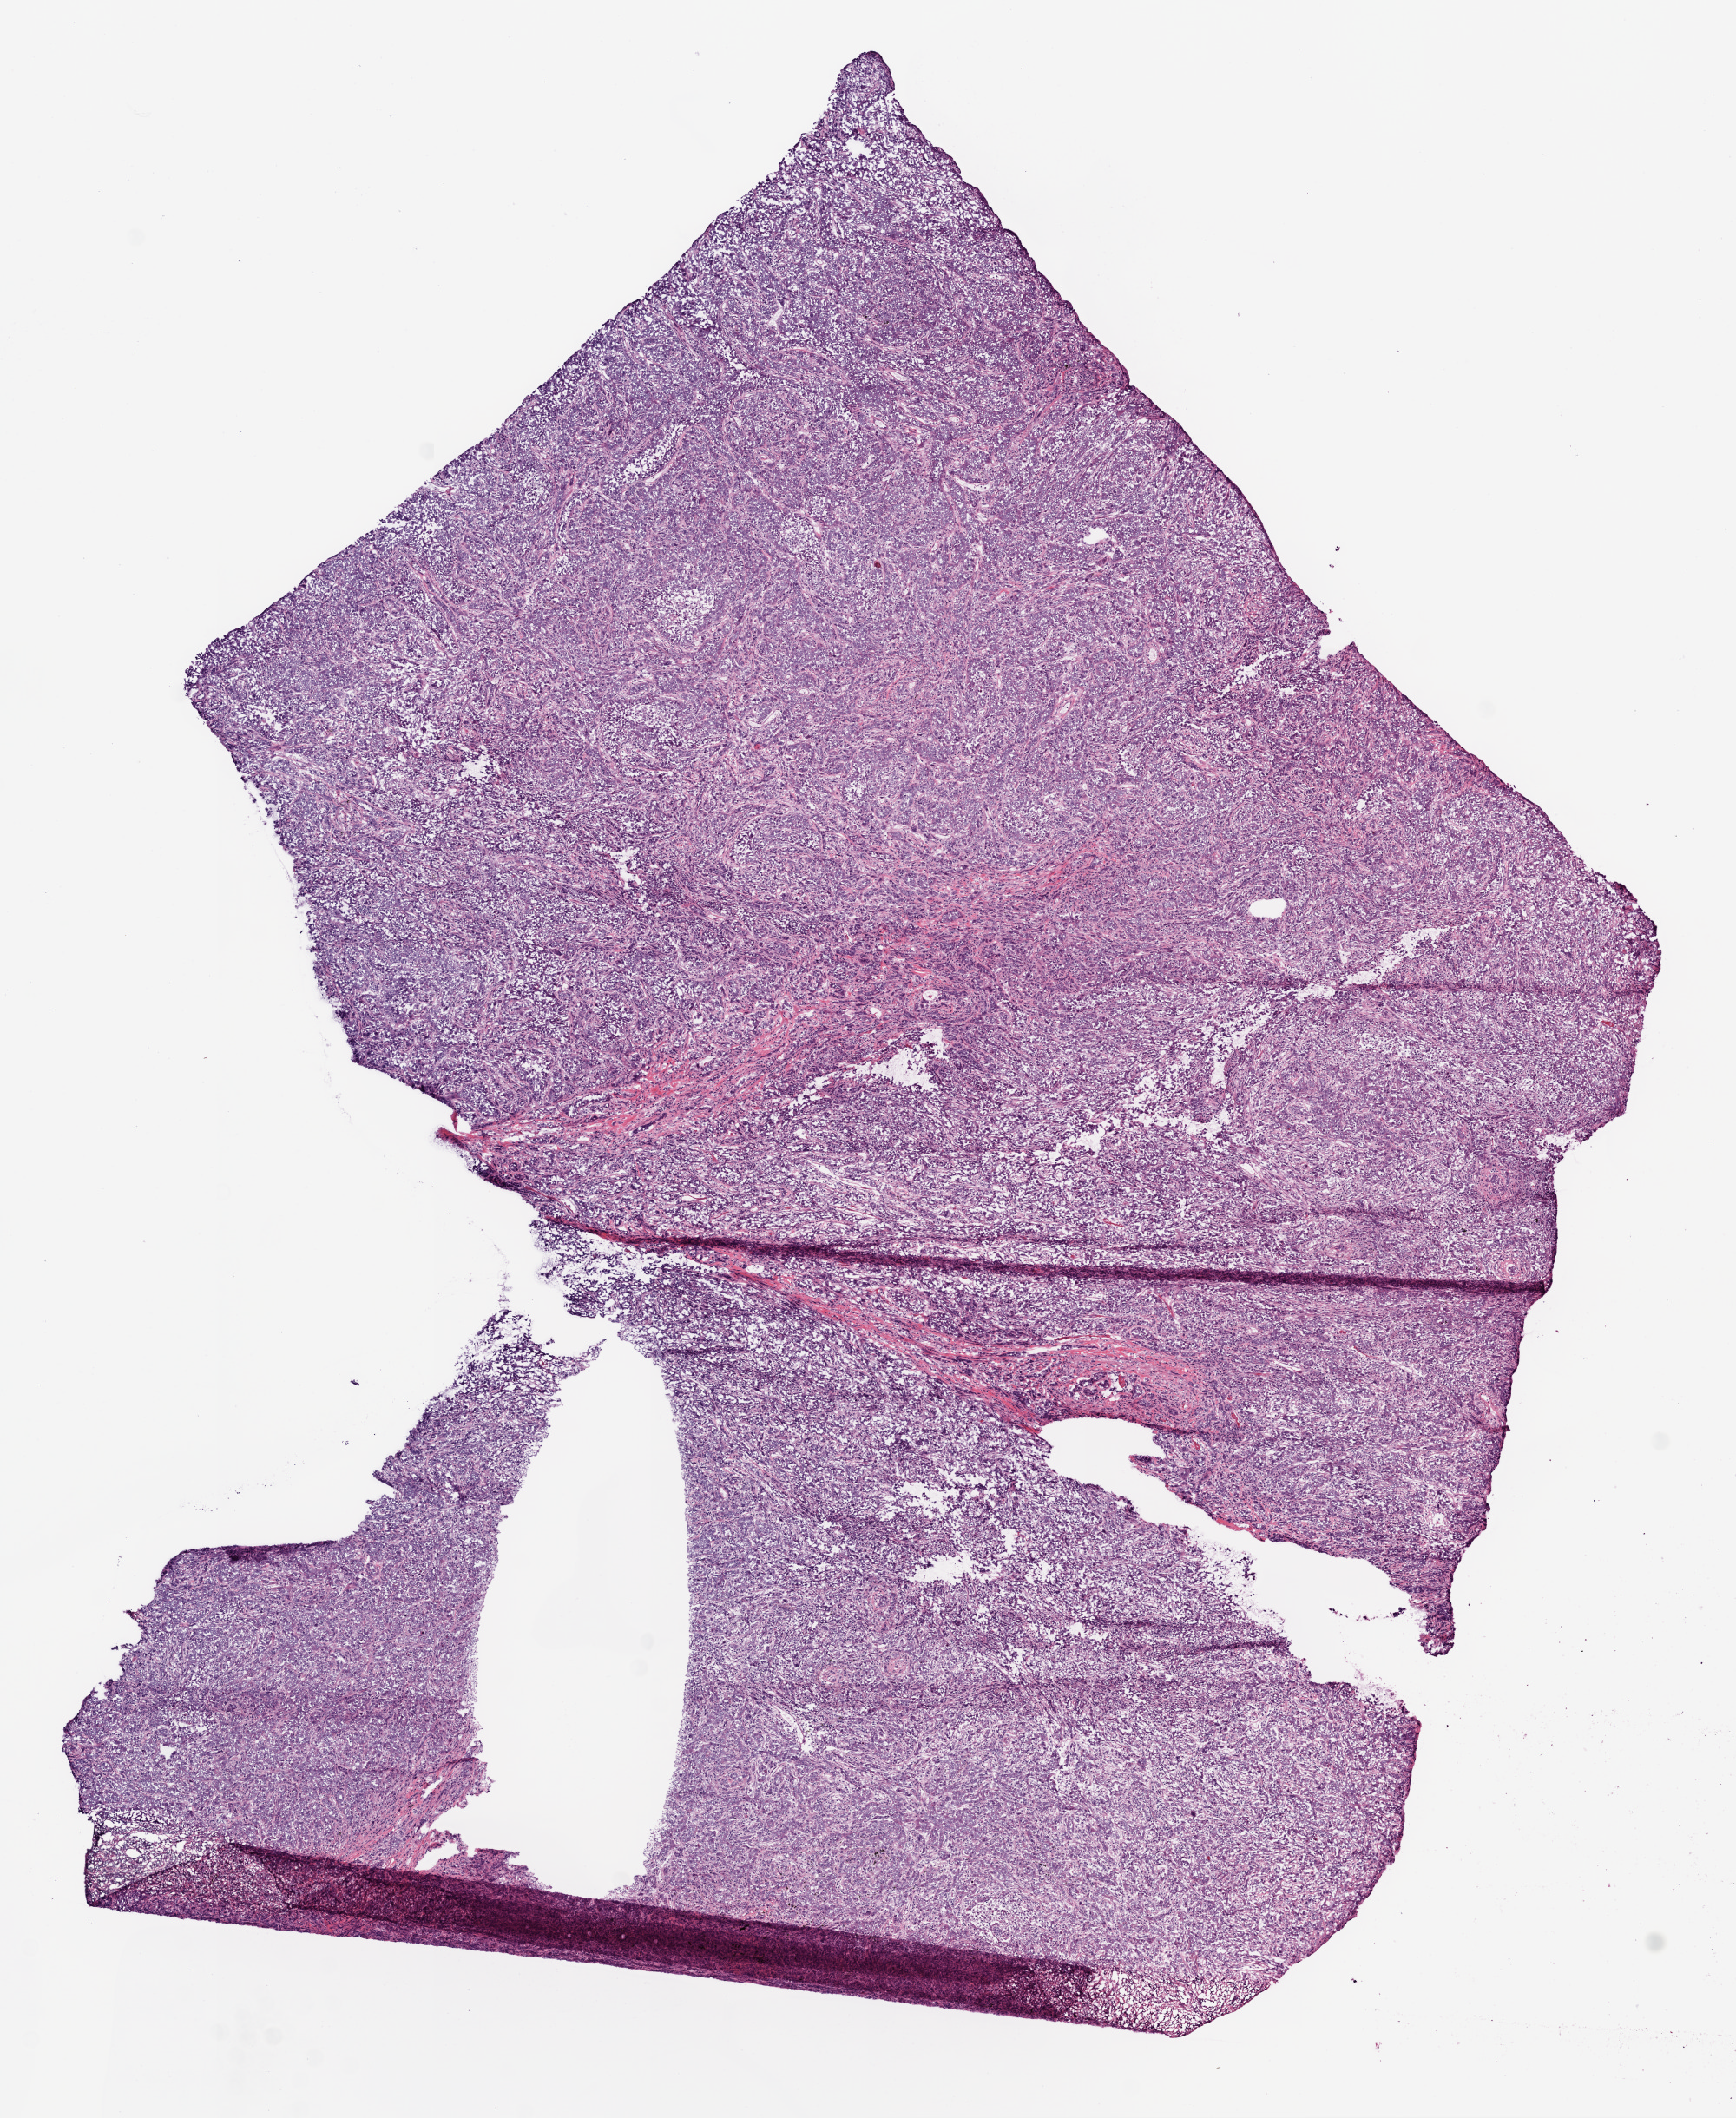
Digitized Hematoxylin and eosin (H&E) stained tissue section (whole slide), a low-resolution overview of the entire scanned area, about 8.0 x 9.8 mm. Frozen section from the bottom of the tissue portion. Lung, primary tumour sample. Male patient; age at initial diagnosis 57 years. Slide review estimates, as recorded: tumour cells 87%, tumour nuclei 75%, normal cells 0%, stromal cells 10%, necrosis 3%.
* histologic diagnosis: Squamous cell carcinoma, NOS (upper lobe, lung)